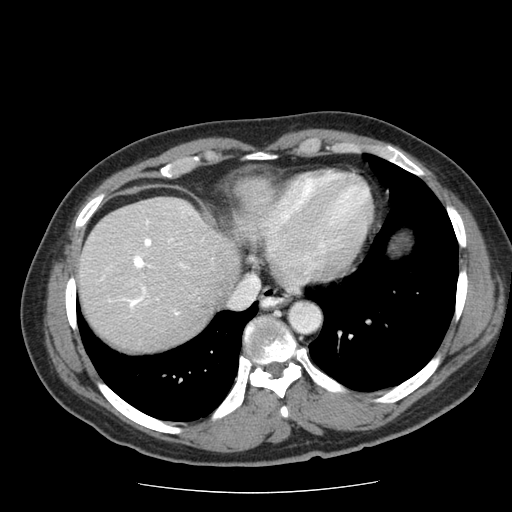
Contrast-enhanced abdominal CT (liver protocol), one axial slice; slice 60 of 85 in the series (ordered by position); reconstruction kernel STANDARD; soft-tissue window (W 400 / L 40 HU); 512 × 512 image matrix, field of view 360 × 360 mm. From the clinical record (not read from this slice): diagnosis: hepatocellular carcinoma (patient treated with transarterial chemoembolisation; whether this scan precedes or follows treatment is not stated here); TNM stage (as recorded): Stage-IIIA; Child-Pugh class: A; tumour differentiation: well differentiated; tumour nodularity: multinodular.
Outlined on this slice (semi-automatically segmented with operator editing):
- liver parenchyma outside the tumour (the mass and vessels are separate outlines, so this box may not span the whole liver): bounding box <78,196,239,350> (left, top, right, bottom; pixels)
- liver vessels: <109,213,190,315>